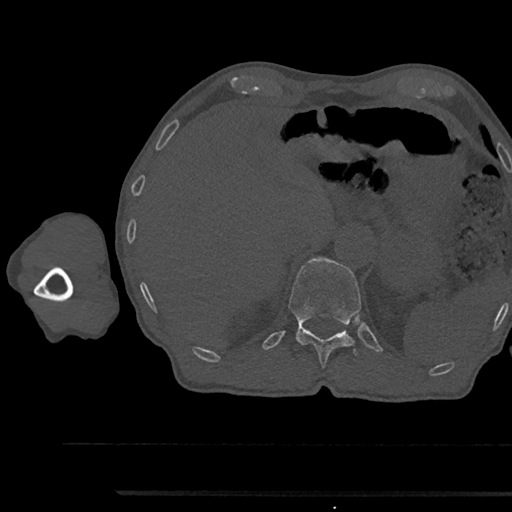
CT including the spine, one axial slice. Position 710 of 797 along the scan axis. Reconstruction kernel Br40s/3. Bone window (W 1800 / L 400 HU). 0.5 mm slice thickness. 512 × 512 image matrix, field of view 367 × 367 mm. Patient: male, 79 years. From the clinical record (not read from this slice): primary cancer: prostate.
Outlined on this slice (semi-automatically segmented with operator editing):
- T12 vertebra: bounding box [x1, y1, x2, y2] px = [289, 258, 361, 368]